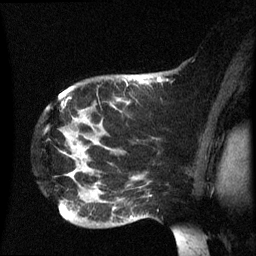
Breast MRI (dynamic contrast-enhanced), one sagittal slice. Slice 48 of 60 in the series (ordered by position). Dynamic contrast-enhanced series, image 2 of 3 at this slice position (ordered by acquisition). 1.5 T. TE 4.2 ms, TR 8.4 ms. 2.5 mm slice thickness. 256 × 256 image matrix, field of view 220 × 220 mm. Female patient, age 49 years.
Annotated regions visible in this slice (semi-automatic segmentation, software-assisted and operator-edited):
- analysis volume of interest (the breast-tissue region the enhancement analysis was run in; not a lesion): bounding box (x1, y1, x2, y2) in pixels: (49, 74, 185, 235)
- tumour enhancement mask (voxels above the 70 % enhancement threshold inside the analysis volume of interest): (131, 82, 144, 219)